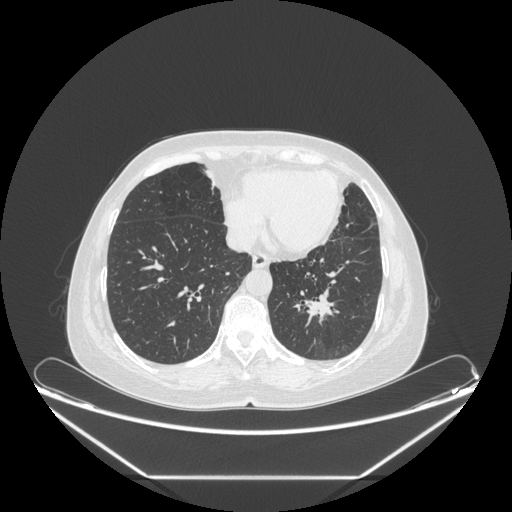
Chest CT, one axial slice; slice 80 of 241 in the series (ordered by position); reconstruction kernel STANDARD; lung window (W 1500 / L -600 HU); 1.25 mm slice thickness; 512 × 512 image matrix, field of view 451 × 451 mm. Patient: female, 63 years. Case-level facts recorded for this patient, not image findings: clinical TNM (as recorded): T1c N0 M0; histopathological grade: G2-3.
Outlined on this slice (bounding box drawn by a radiologist):
- lung tumour (recorded histology: adenocarcinoma): box from (x=303, y=286) to (x=338, y=332) px